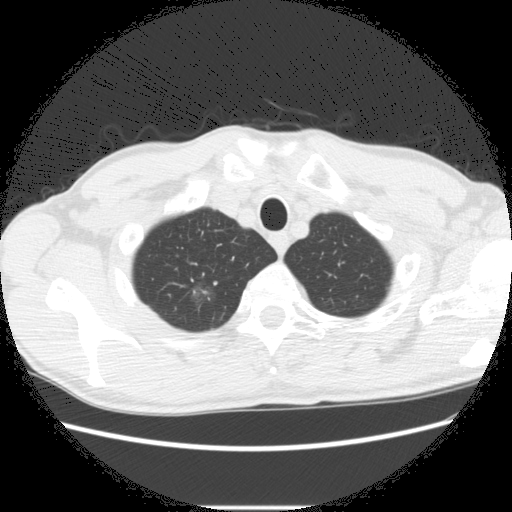
Low-dose screening chest CT, one axial slice; slice 253 of 282 in the series (ordered by position); lung window (W 1500 / L -600 HU); 2.5 mm slice thickness; 512 × 512 image matrix, field of view 360 × 360 mm.
Structures marked on this image (manually delineated by an expert):
- lesion 2 (nodule, upper lobe of right lung): bounding box [x1, y1, x2, y2] px = [192, 282, 216, 304]